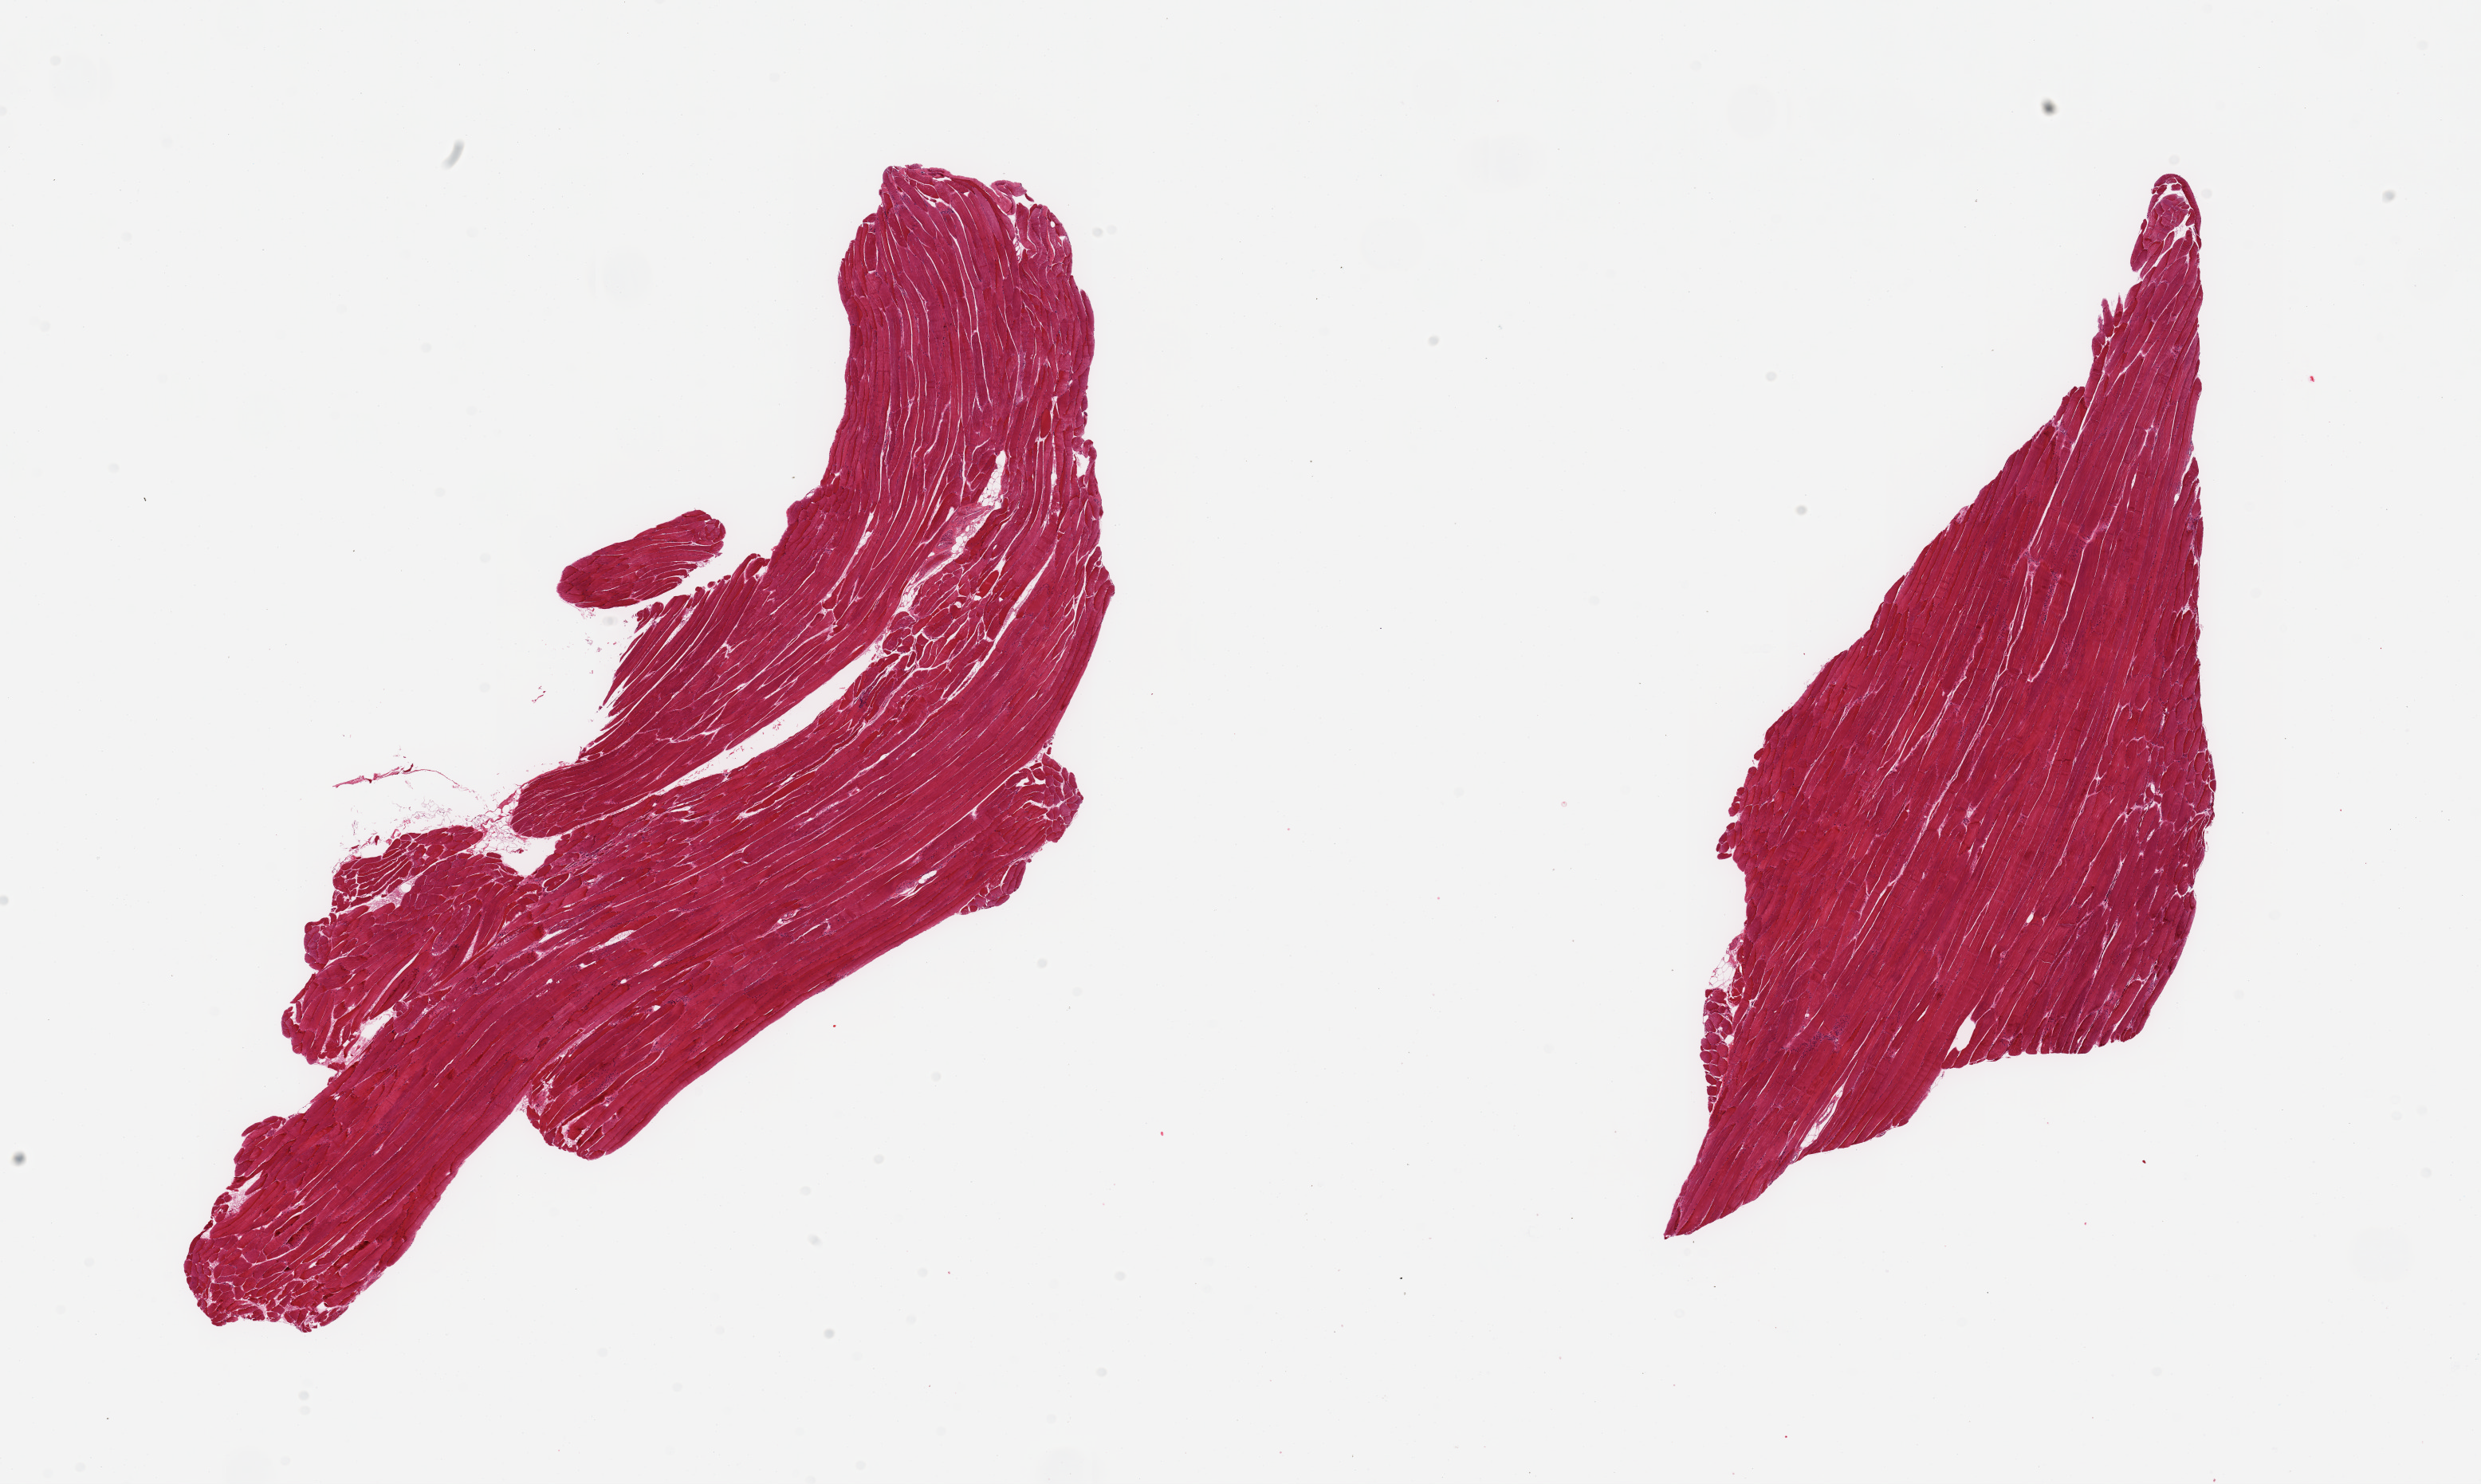
Digitized H&E-stained section, low-resolution overview of the scanned area, about 24.6 x 14.7 mm, PAXgene-fixed, paraffin-embedded tissue, section of skeletal muscle (target tissue), tissue donor sample. Donor: male.
Reviewer comment on this tissue sample: 2 pieces, trace interstitital fat.